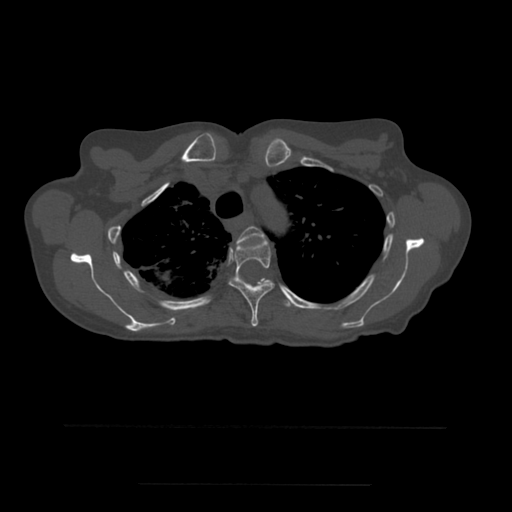
CT including the spine, one axial slice. Slice 407 of 544 in the series (ordered by position). Bone window (W 1800 / L 400 HU). 1.25 mm slice thickness. 512 × 512 image matrix, field of view 350 × 350 mm. Patient age 58 years. Case-level facts recorded for this patient, not image findings: primary cancer: lung.
Outlined on this slice (semi-automatically segmented with operator editing):
- T3 vertebra: bounding box <237,226,267,246> (left, top, right, bottom; pixels)
- T4 vertebra: <229,239,275,327>
- T5 vertebra: <239,278,296,307>